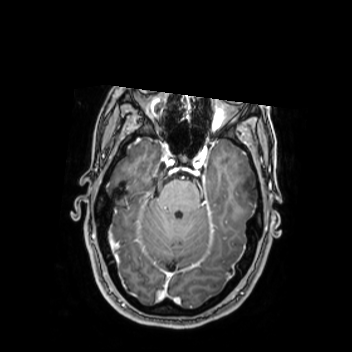
Brain MRI from a brain-tumour surgery series, one axial slice. T1-weighted post-contrast. 0.9 mm slice thickness. 352 × 352 image matrix, field of view 280 × 280 mm. From the clinical record (not read from this slice): histopathology: Oligodendroglioma; WHO grade: 2; IDH mutation: yes; tumour location: Left Middle Temporal Gyrus.
Outlined on this slice (outlined manually by an expert reader):
- tumour: bounding box [x1, y1, x2, y2] px = [224, 168, 262, 206]